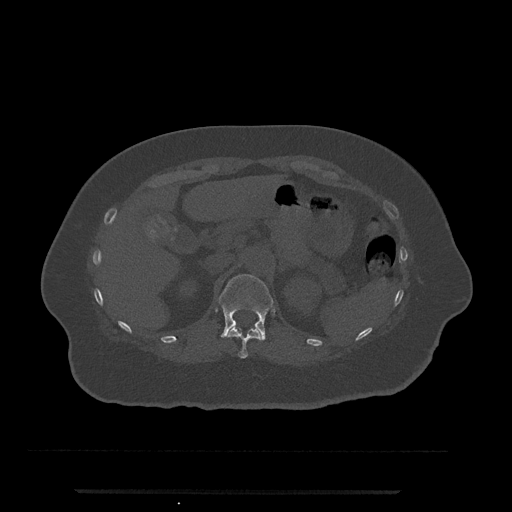
CT including the spine, one axial slice; position 193 of 797 along the scan axis; 120 kVp; bone window (W 1800 / L 400 HU); 0.5 mm slice thickness; 512 × 512 image matrix, field of view 440 × 440 mm. Female patient, age 51 years. Case-level facts recorded for this patient, not image findings: primary cancer: neuro; vertebrae with lytic lesions (as recorded): T8.
Outlined on this slice (semi-automatic segmentation, software-assisted and operator-edited):
- T11 vertebra: bounding box [x1, y1, x2, y2] px = [226, 327, 261, 359]
- T12 vertebra: [219, 274, 274, 341]